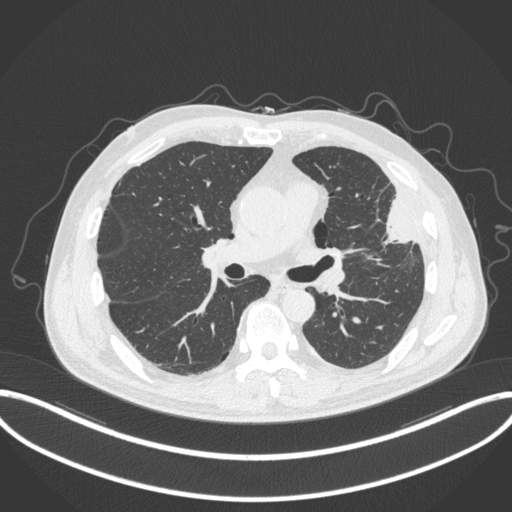
Chest CT, one axial slice; position 188 of 382 along the scan axis; reconstruction kernel B31f; lung window (W 1500 / L -600 HU); 1 mm slice thickness; 512 × 512 image matrix, field of view 415 × 415 mm. Male patient, age 64 years. Case-level facts recorded for this patient, not image findings: clinical TNM (as recorded): T4 N1 M0; histopathological grade: G3.
Structures marked on this image (bounding box drawn by a radiologist):
- lung tumour (recorded histology: adenocarcinoma): bounding box [x1, y1, x2, y2] px = [373, 193, 418, 246]